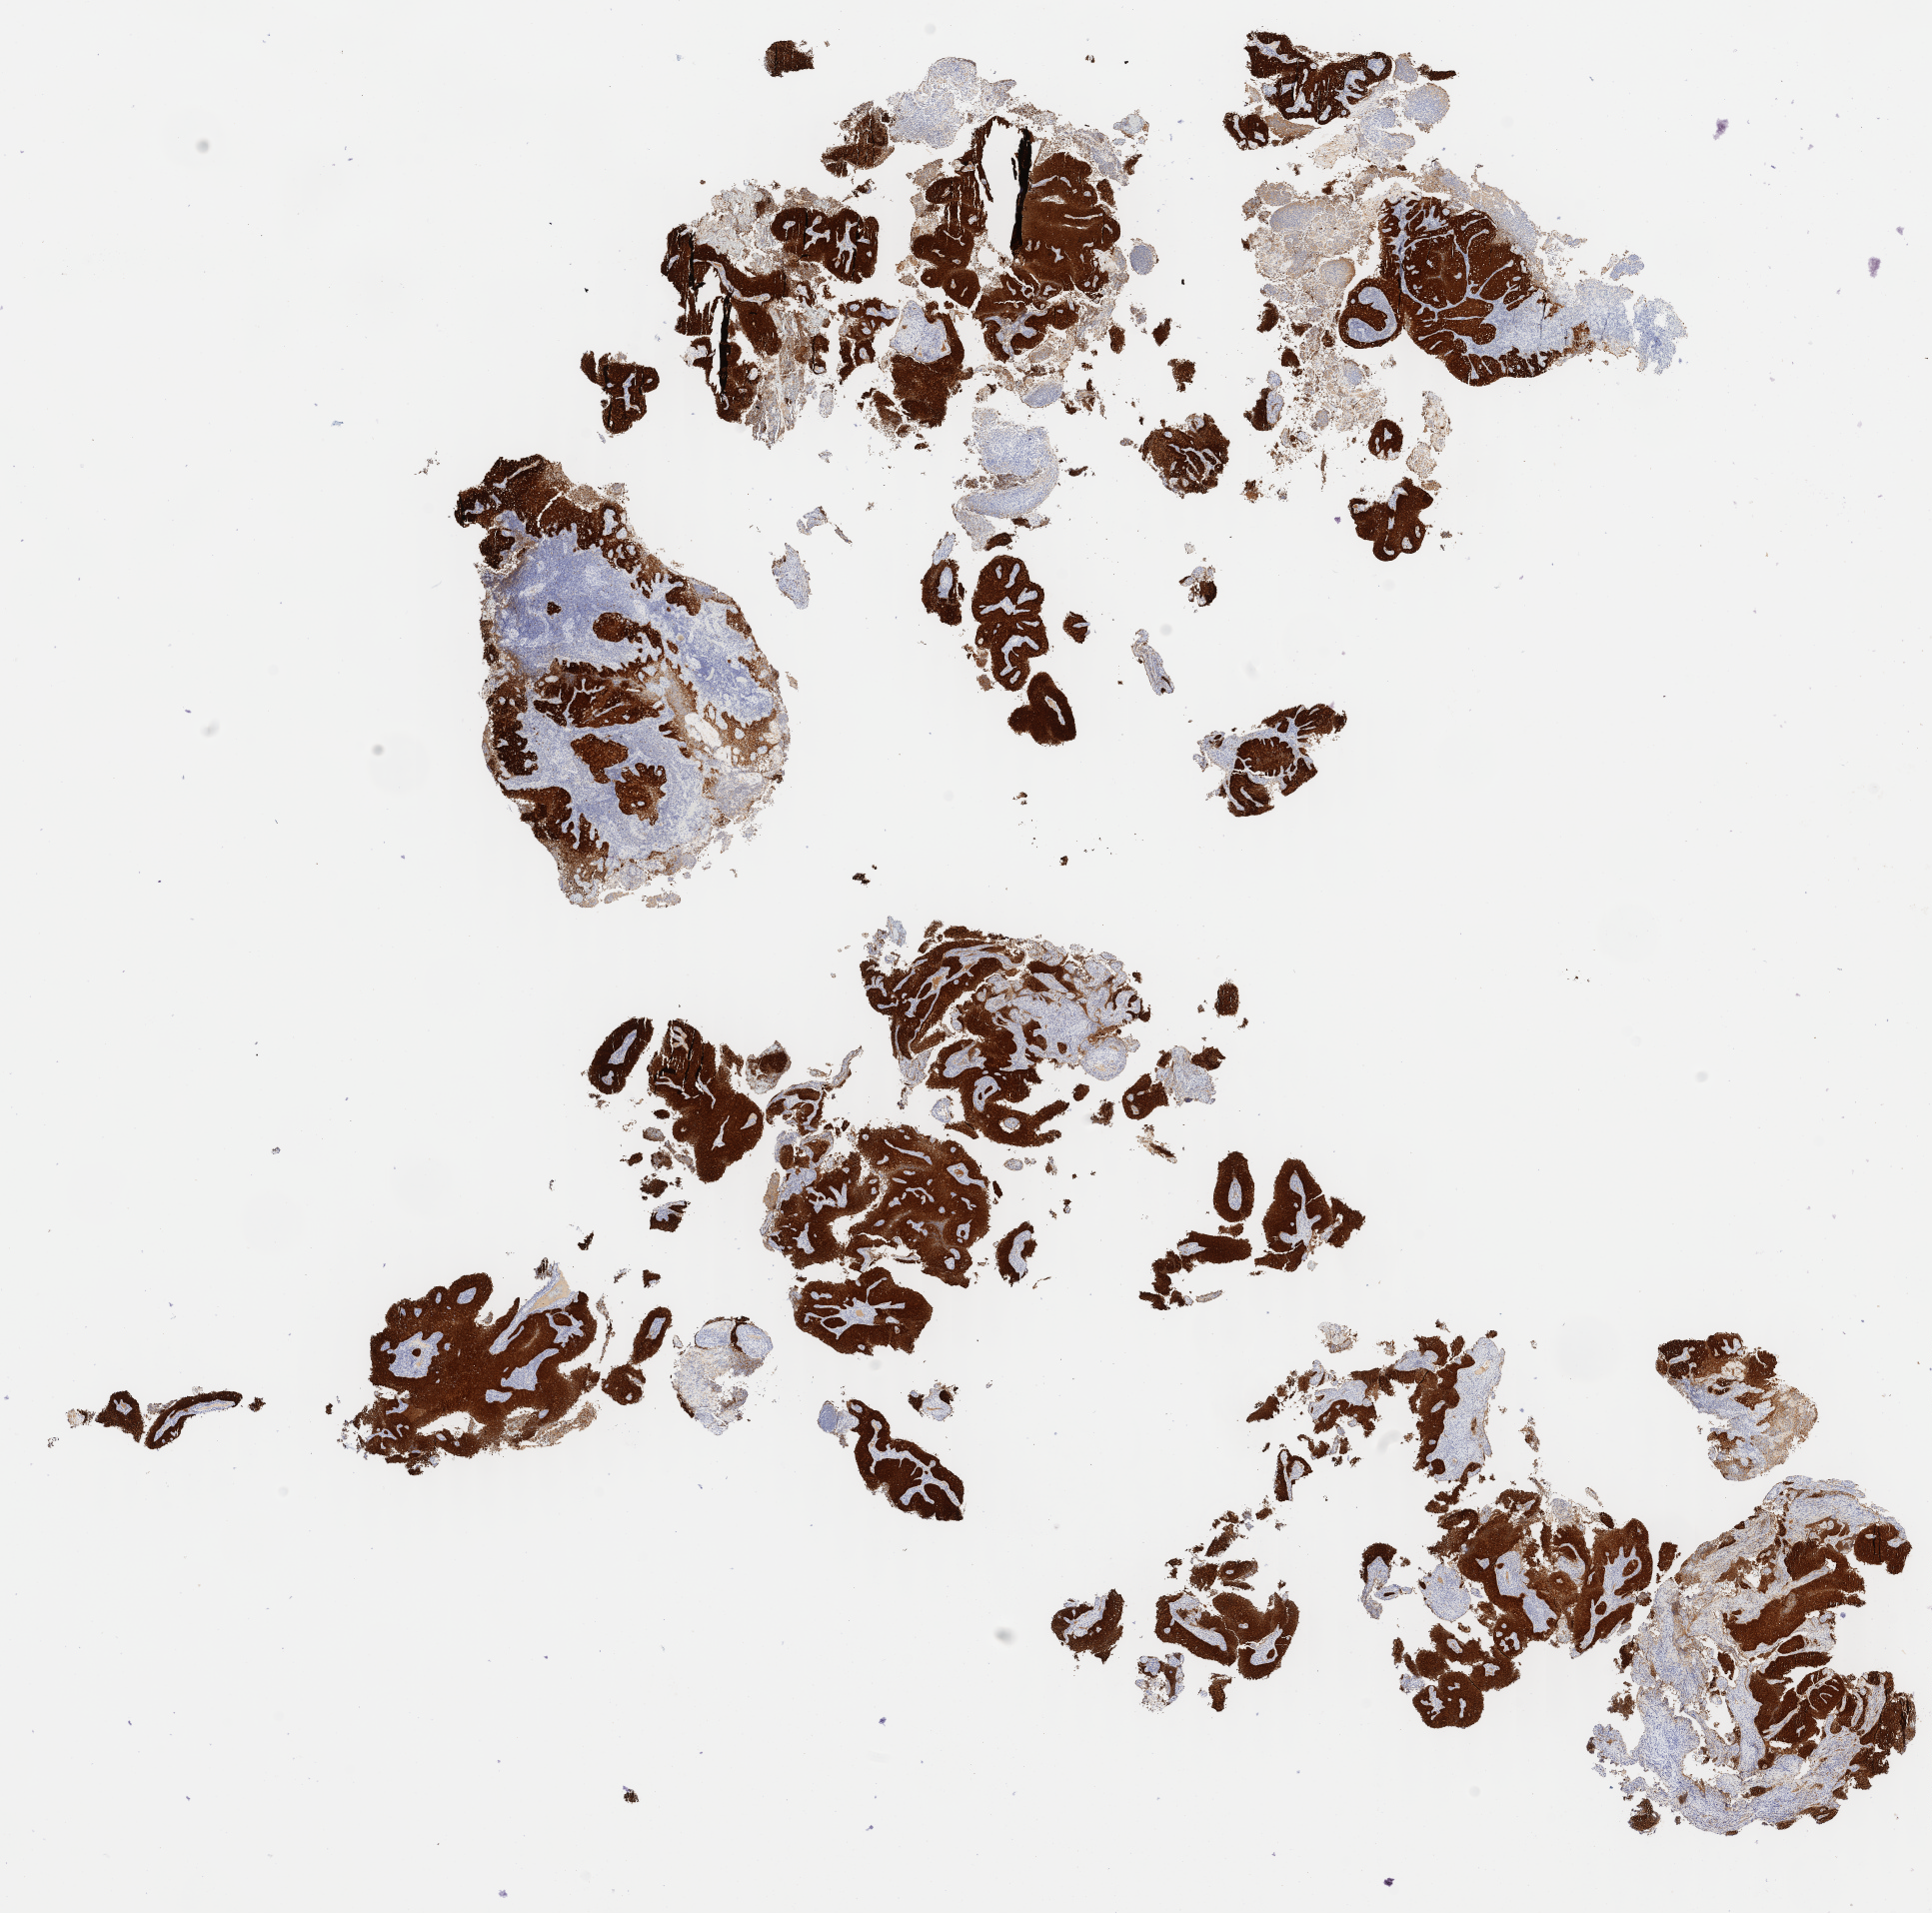
Whole-slide image, immunohistochemical stain for p16 (p16INK4a) — shown as a low-resolution overview of the whole scanned area (about 15.4 x 15.2 mm); tumor tissue; anatomic site: cervix. Patient: female, 40 years old.
* diagnosis: Adenocarcinoma, NOS